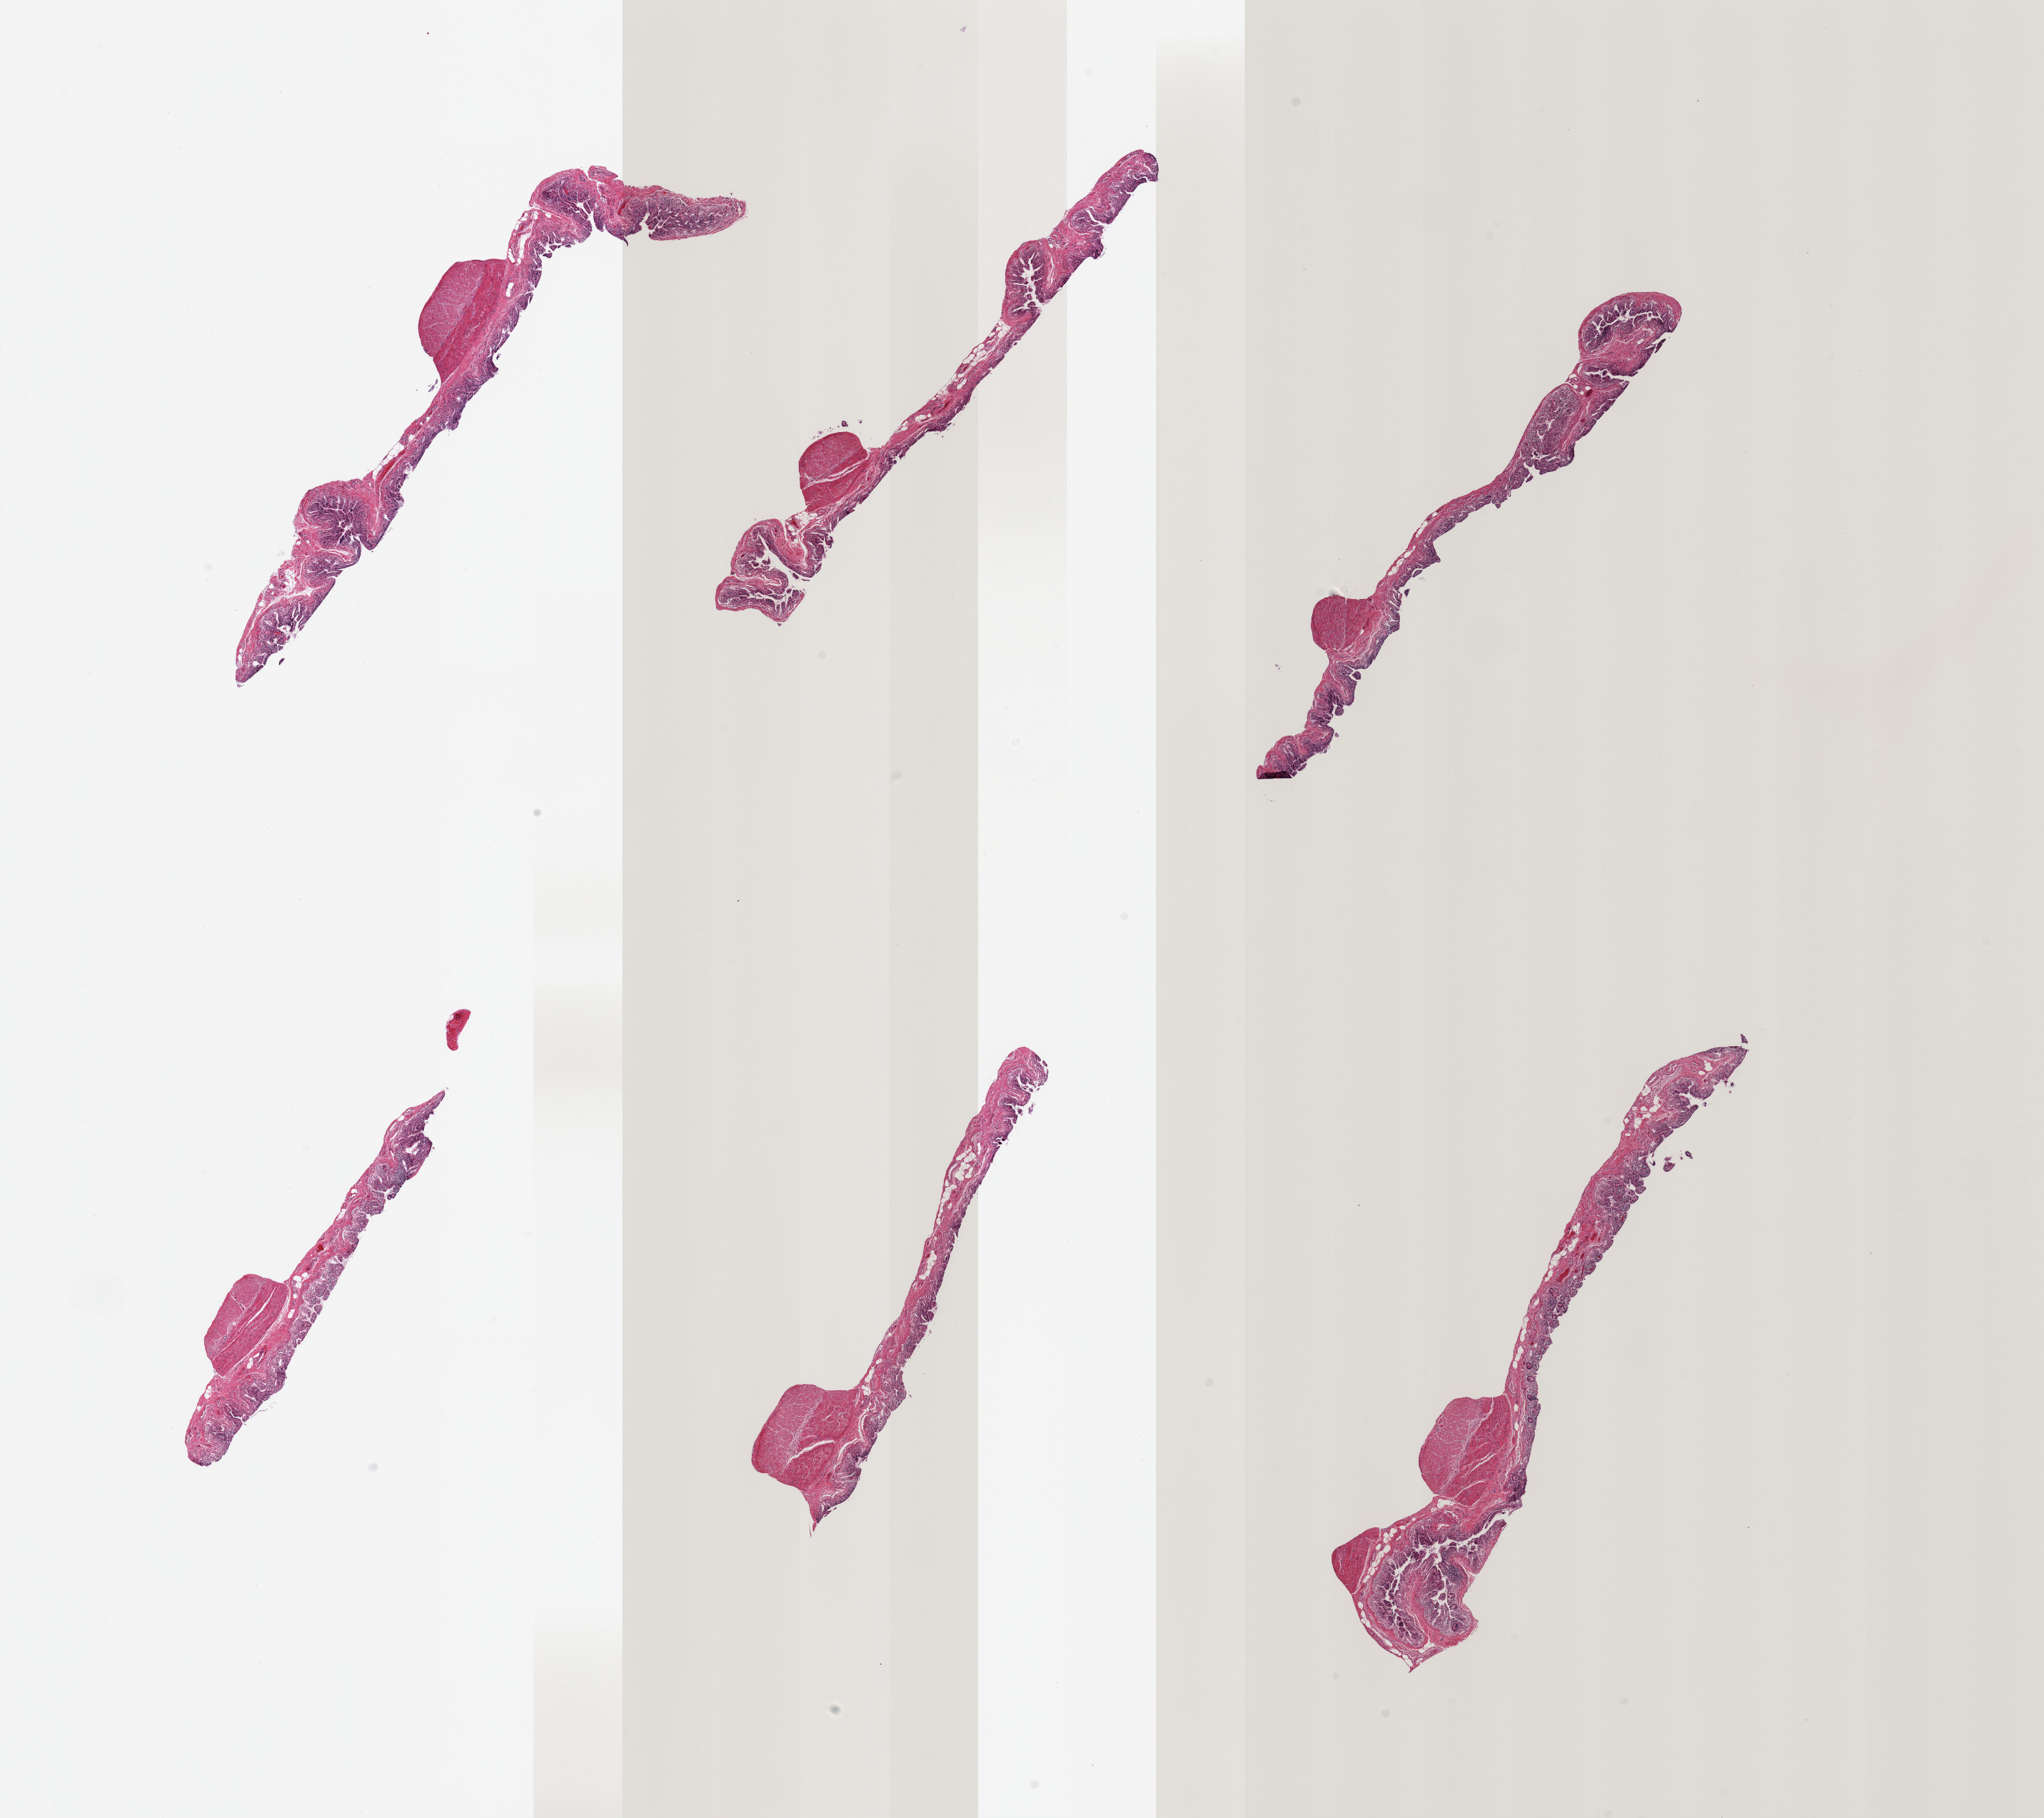
Digitized hematoxylin and eosin (H&E)-stained section, a low-resolution overview of the entire scanned area, about 22.6 x 20.1 mm (from a 20x scan); PAXgene-fixed paraffin-embedded (PFPE) section; sampled site (target tissue): ileum; donor tissue sample. Female donor.
Pathologist's review note for this sample: 6 pieces, mucosa largely sloughed, <5% target lymphoid aggregates.